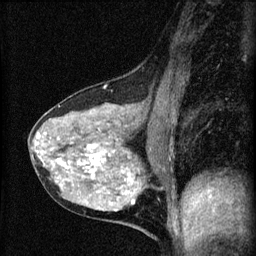
Breast MRI (dynamic contrast-enhanced), one sagittal slice. Position 27 of 60 along the scan axis. Dynamic contrast-enhanced series, image 2 of 4 at this slice position (ordered by acquisition). 1.5 T. TE 4.2 ms, TR 8.2 ms. 2 mm slice thickness. 256 × 256 image matrix, field of view 180 × 180 mm. Patient: female, 41 years.
Structures marked on this image (semi-automatic segmentation, software-assisted and operator-edited):
- analysis volume of interest (the breast-tissue region the enhancement analysis was run in; not a lesion): bounding box [x1, y1, x2, y2] px = [29, 91, 166, 210]
- tumour enhancement mask (voxels above the 70 % enhancement threshold inside the analysis volume of interest): [35, 144, 134, 204]